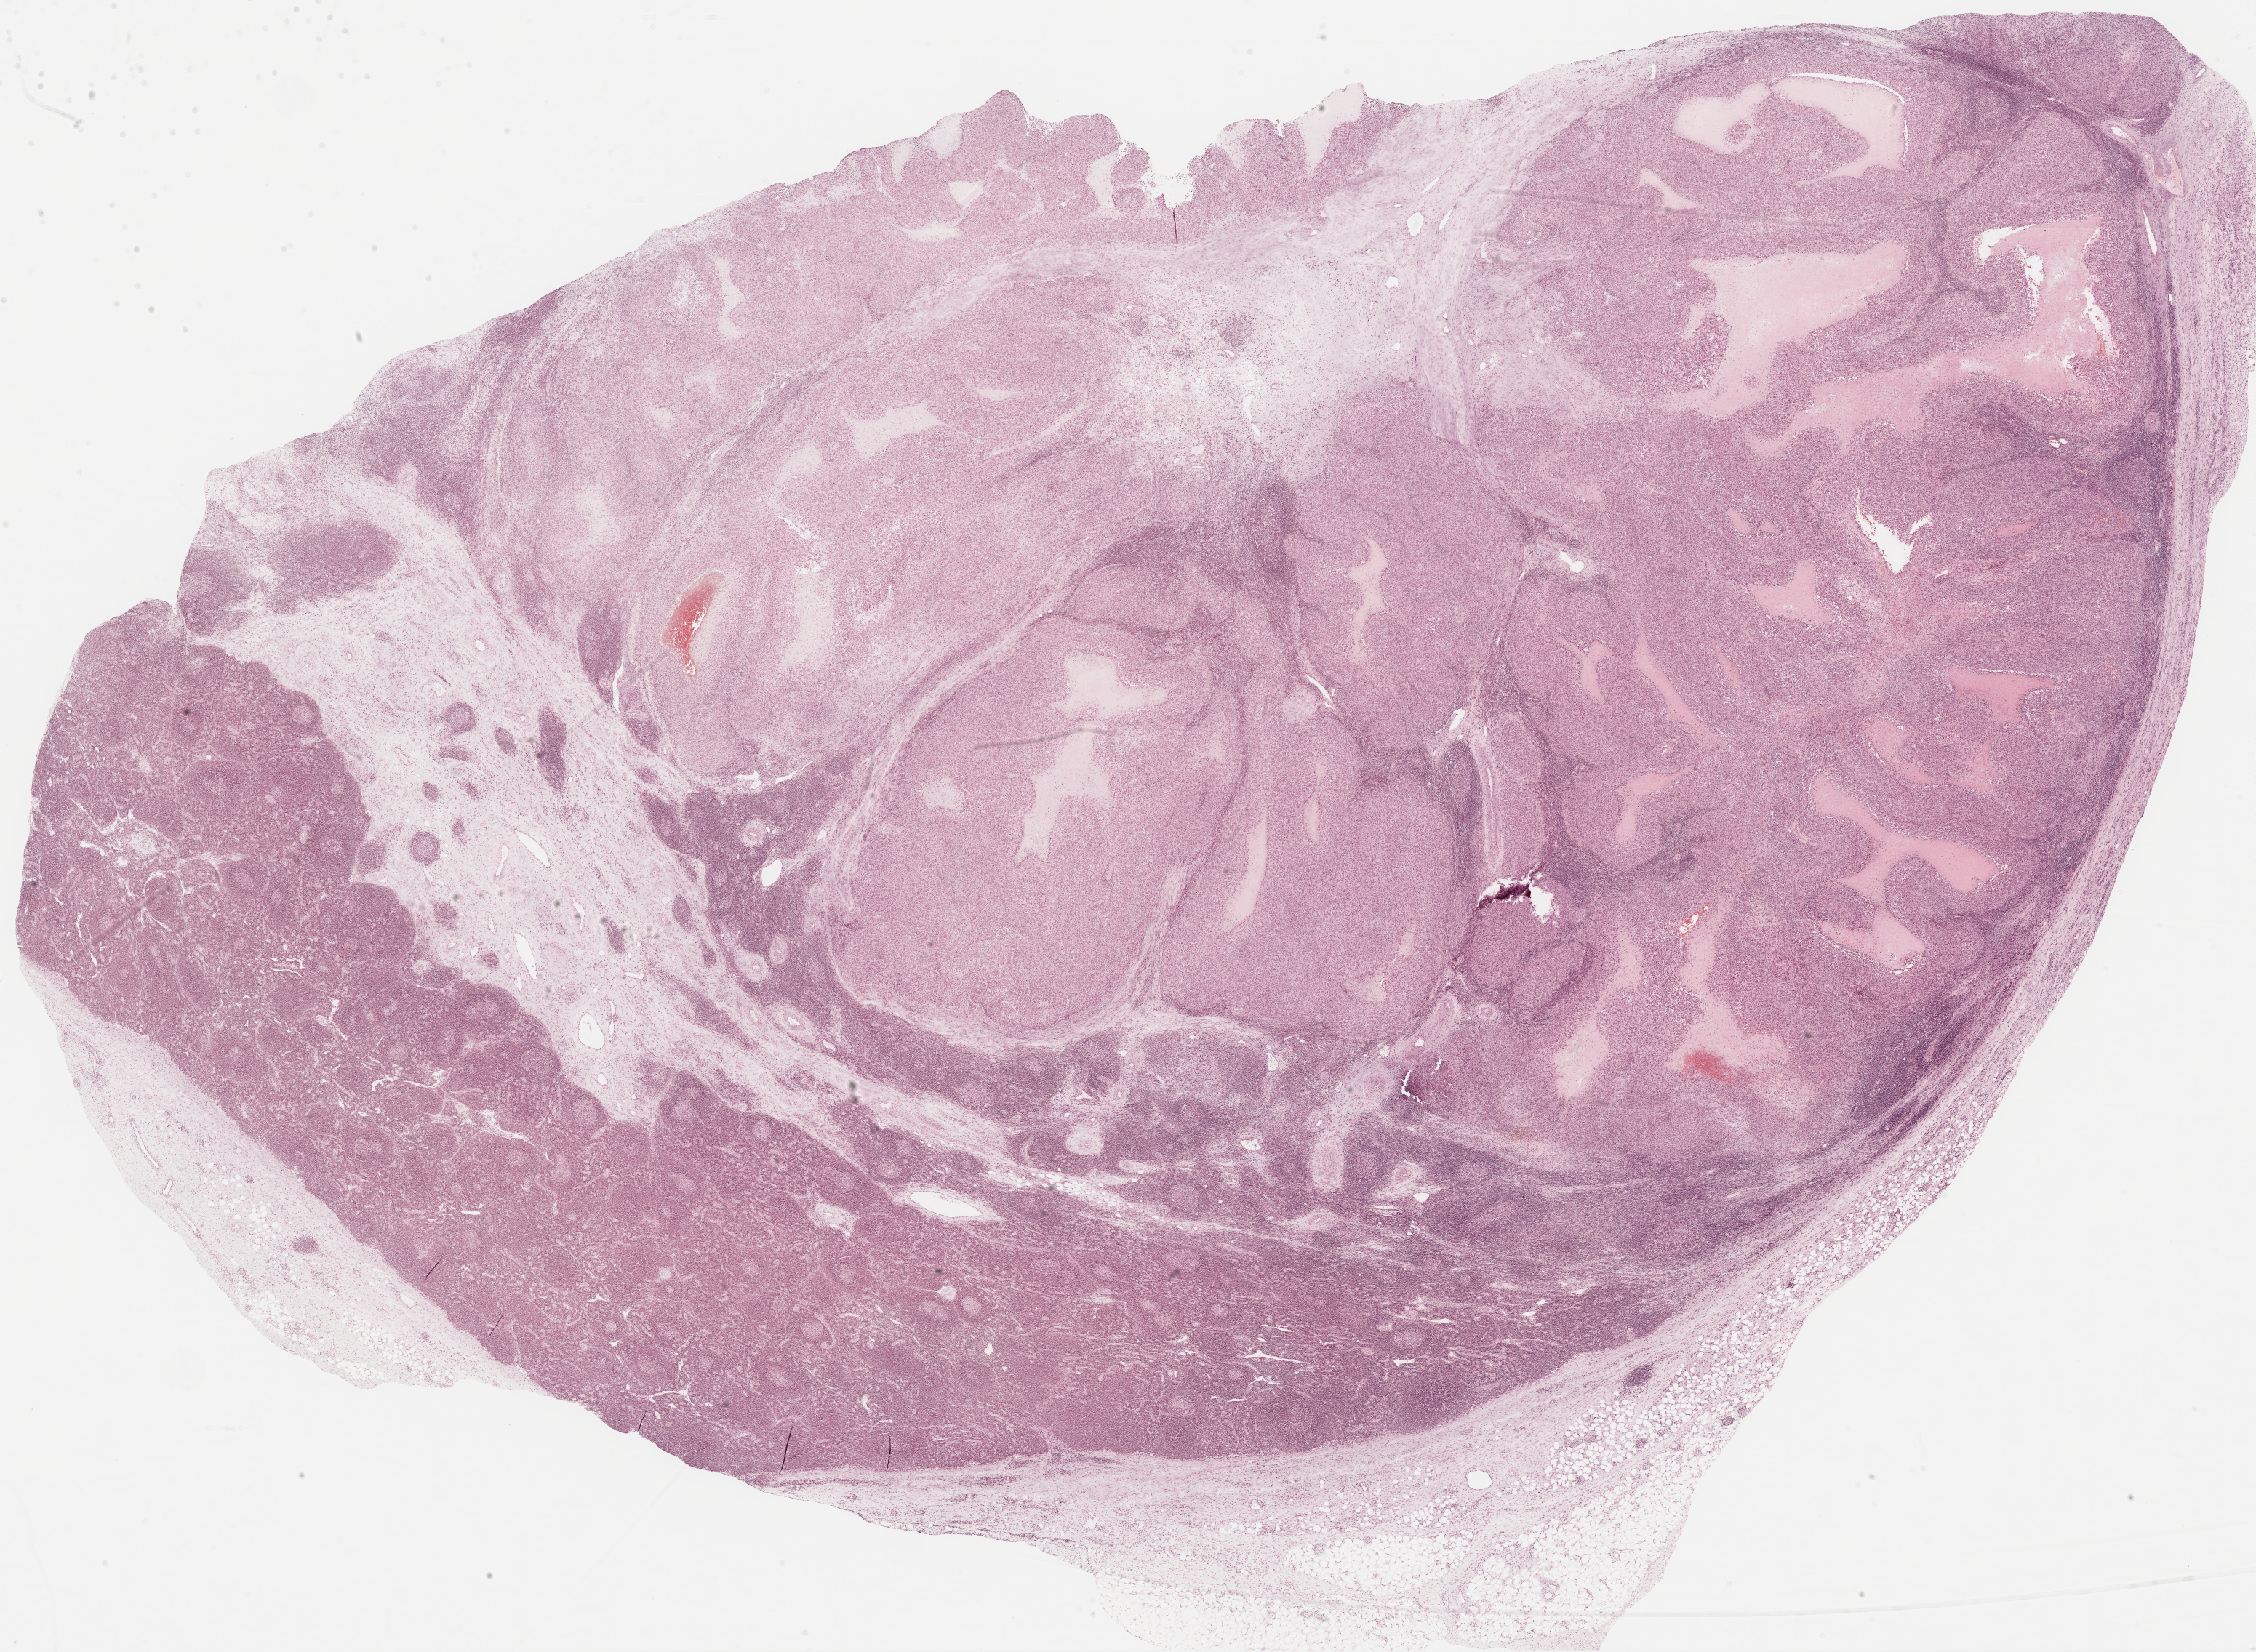
Whole-slide histology image, H&E, whole scanned area (about 25.0 x 18.3 mm, slide scanned at 20x) shown as a low-resolution overview; FFPE section; metastatic tumour sample, sampled site: lymph nodes of inguinal region or leg. Female patient; age at initial diagnosis 57 years.
* this section: metastatic tumour tissue
* patient diagnosis: Malignant melanoma, NOS